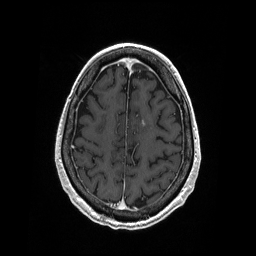
Brain MRI from a brain-tumour surgery series, one axial slice; position 63 of 208 along the scan axis; T1-weighted post-contrast; 1 mm slice thickness; 256 × 256 image matrix, field of view 256 × 256 mm. From the clinical record (not read from this slice): histopathology: Primary diffuse large B-cell lymphoma; tumour location: Left Corpus Callosum (Frontal).
Outlined on this slice (expert manual segmentation):
- tumour: box from (x=142, y=120) to (x=146, y=127) px